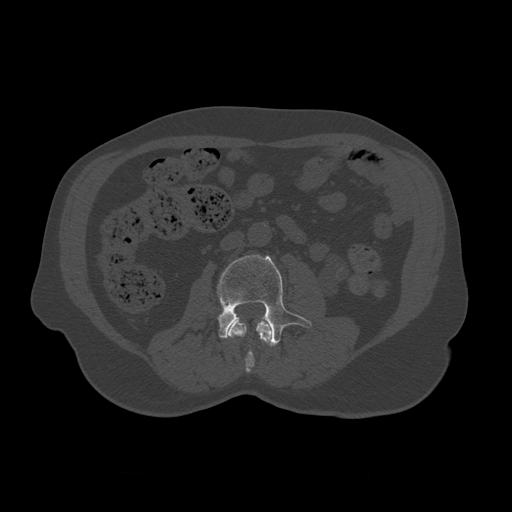
CT including the spine, one axial slice; slice 311 of 450 in the series (ordered by position); reconstruction kernel STANDARD; bone window (W 1800 / L 400 HU); 512 × 512 image matrix. Patient age 75 years. Case-level facts recorded for this patient, not image findings: primary cancer: prostate.
Outlined on this slice (semi-automatically segmented with operator editing):
- L2 vertebra: bounding box [x1, y1, x2, y2] px = [228, 317, 273, 373]
- L3 vertebra: [217, 255, 313, 347]